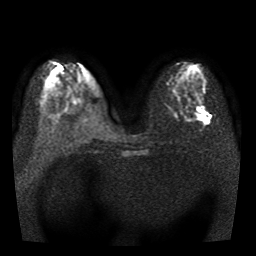
Breast MRI, one axial slice. Position 15 of 41 along the scan axis. Diffusion-weighted series; image 2 of 3 stored at this slice position (different b-values; order by instance number). 1.5 T. 5 mm slice thickness. 256 × 256 image matrix. Female patient.
Outlined on this slice (expert manual segmentation):
- tumour on diffusion-weighted imaging: bounding box <200,108,209,123> (left, top, right, bottom; pixels)